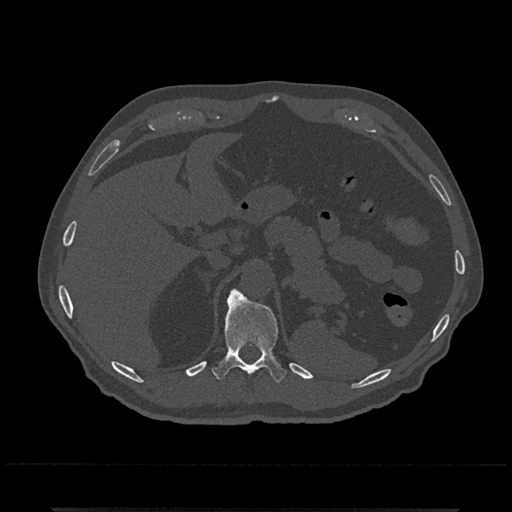
CT including the spine, one axial slice. Slice 495 of 797 in the series (ordered by position). Reconstruction kernel Br40s/3. 120 kVp. Bone window (W 1800 / L 400 HU). 0.5 mm slice thickness. 512 × 512 image matrix, field of view 393 × 393 mm. Male patient, age 67 years. Case-level facts recorded for this patient, not image findings: primary cancer: prostate.
Outlined on this slice (semi-automatic segmentation, software-assisted and operator-edited):
- T11 vertebra: bounding box [x1, y1, x2, y2] px = [212, 286, 287, 383]